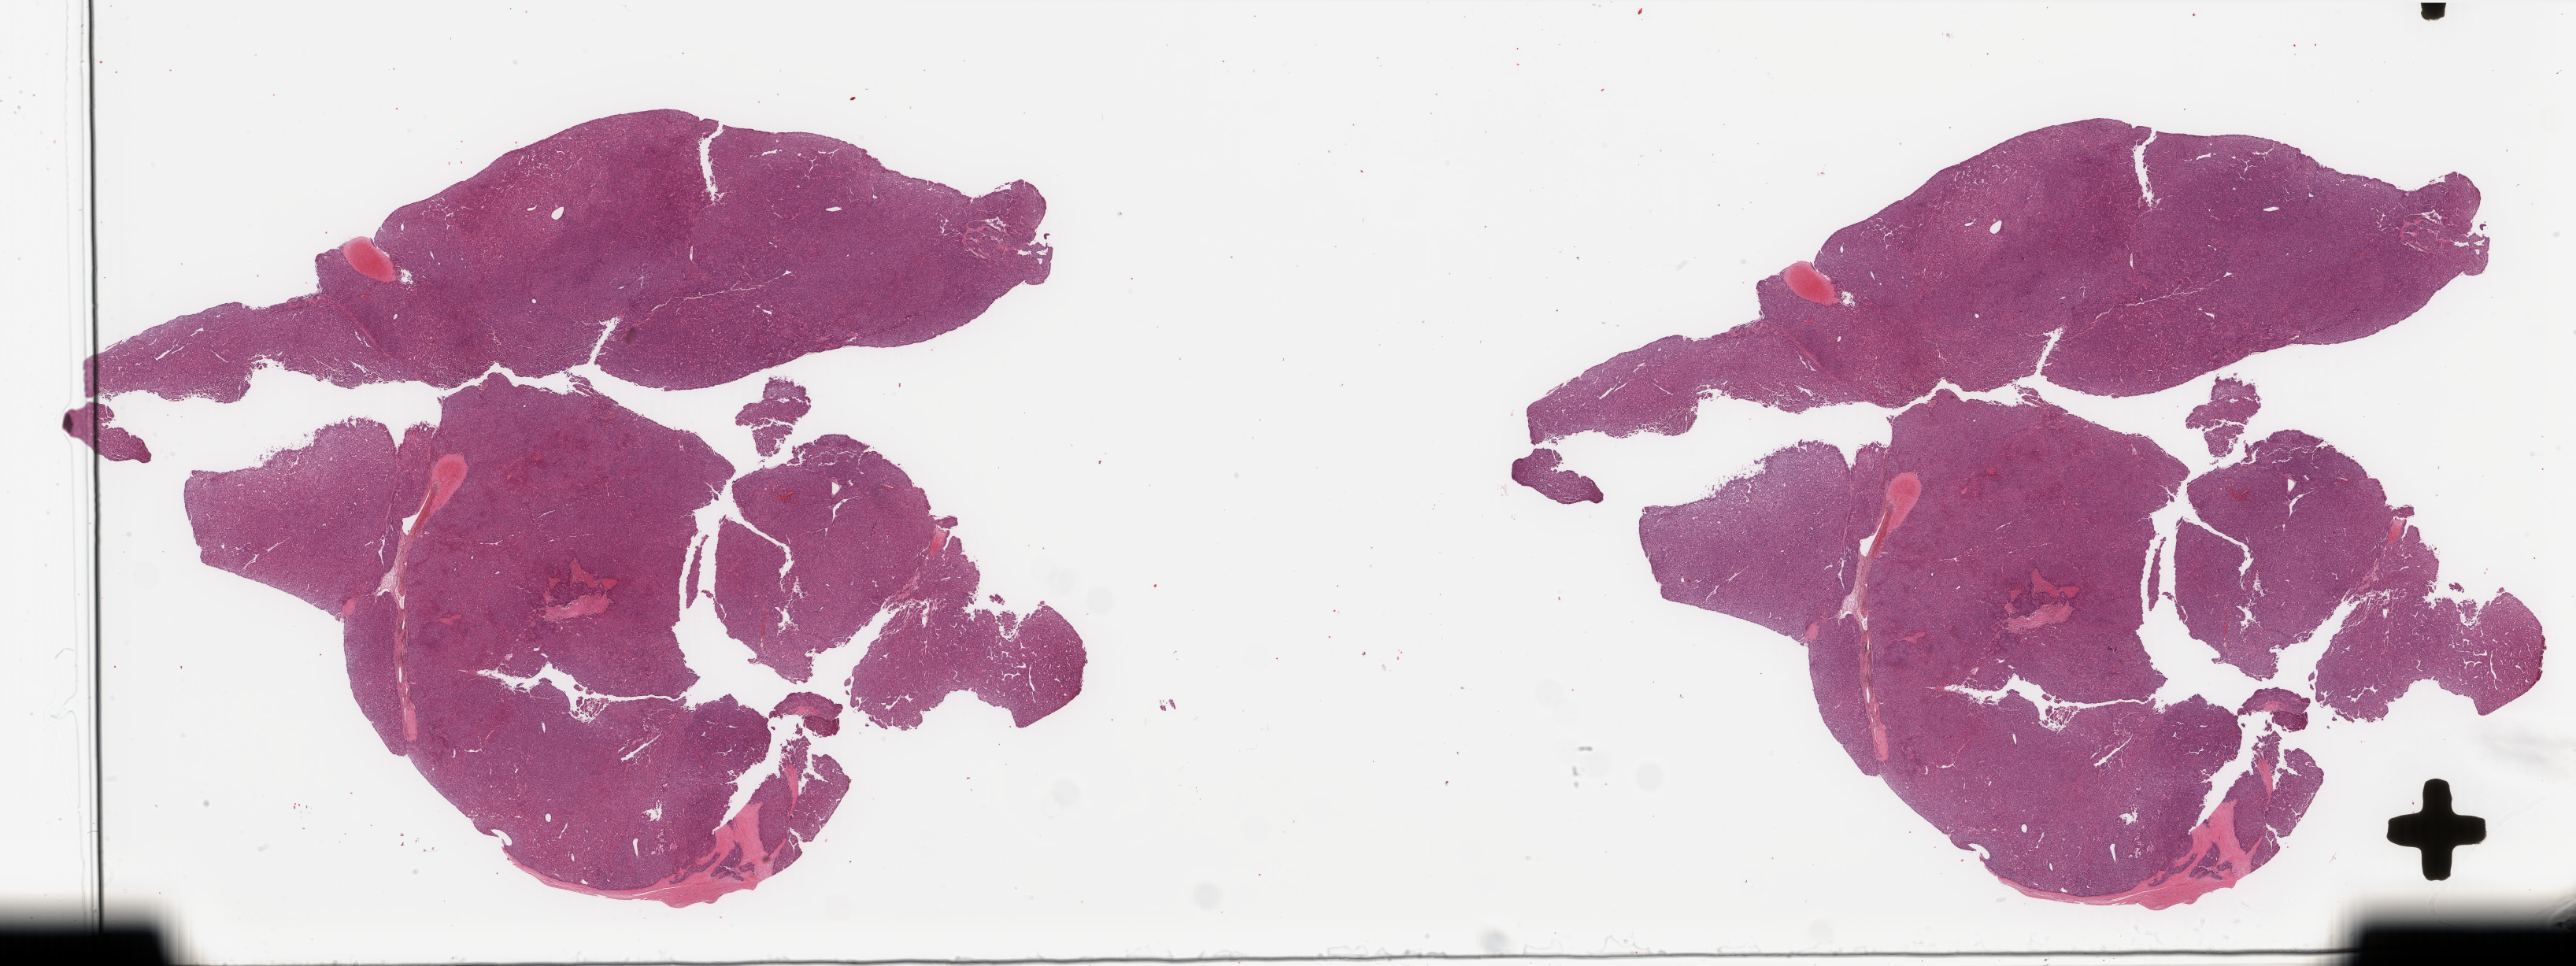
Digitized Hematoxylin and eosin (H&E) stained tissue section (whole slide) — shown as a low-resolution overview of the whole scanned area (about 51.8 x 19.4 mm, acquisition: 40x scan), formalin-fixed paraffin-embedded (FFPE) diagnostic section, primary tumour sample from the liver. Patient: male, age at initial diagnosis 69 years. Histologic grade: G3 (poorly differentiated).
AJCC pathologic stage: IIIA (7th edition). Histologic diagnosis: Hepatocellular carcinoma, NOS.